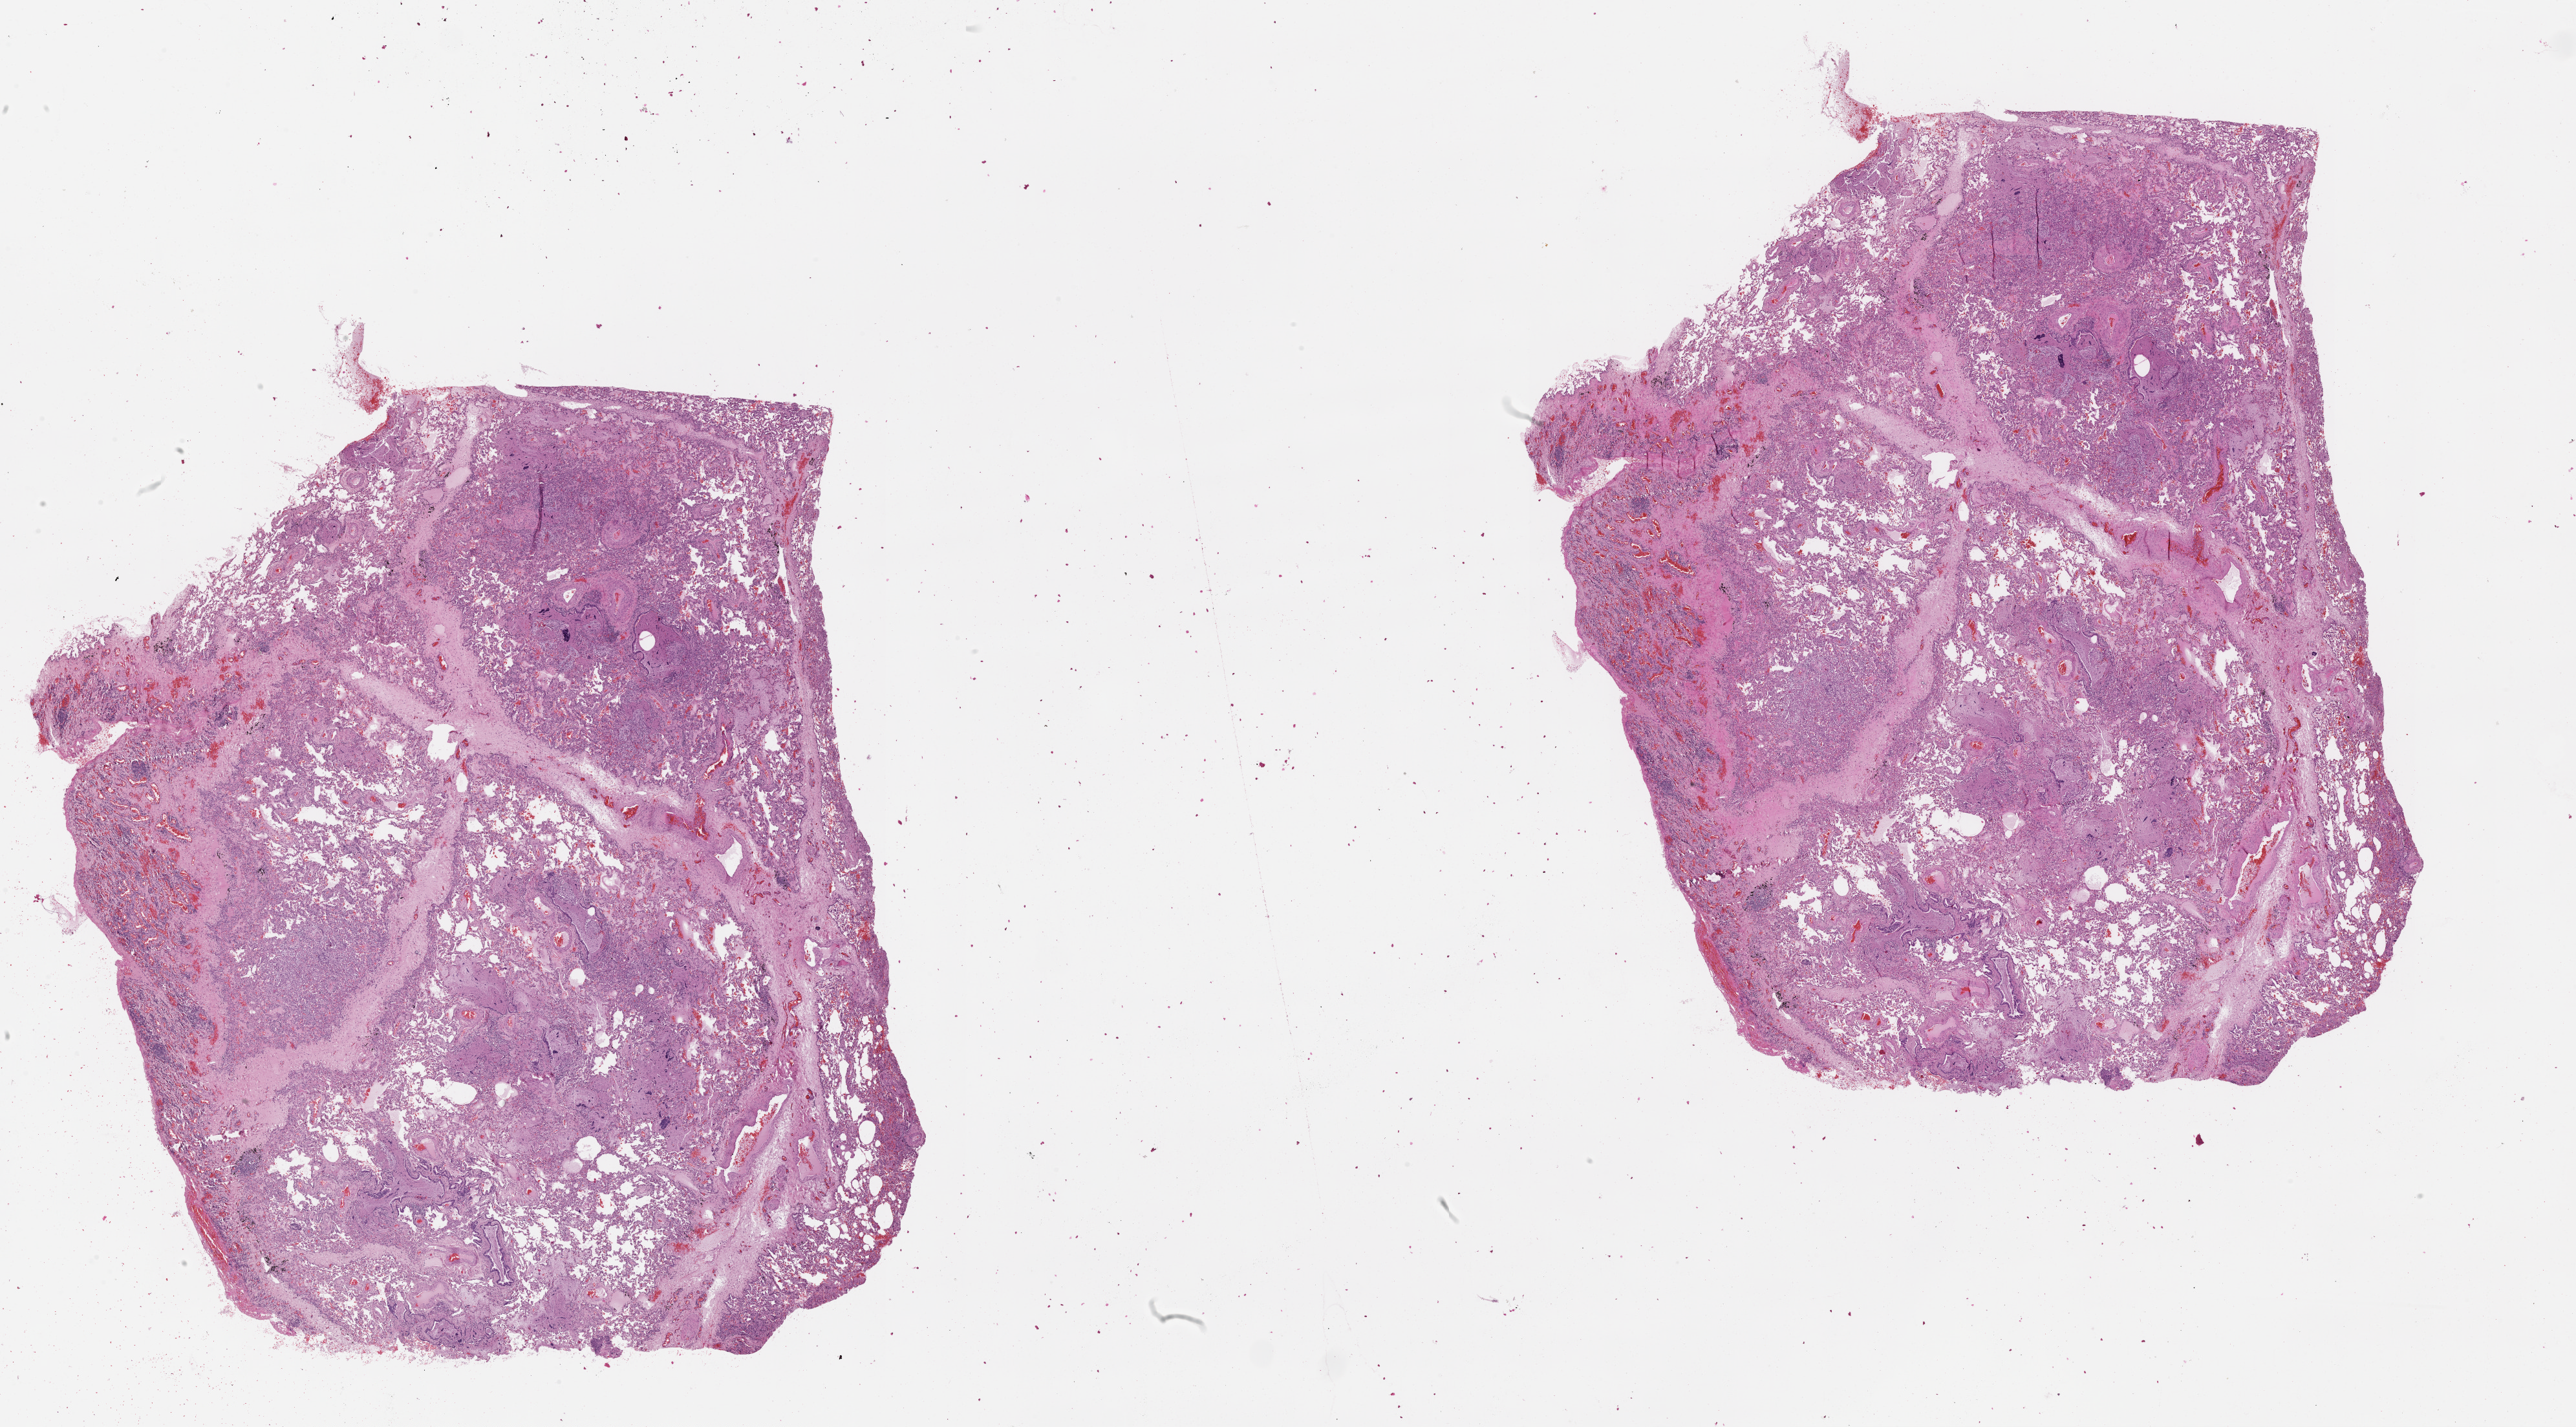
Whole-slide histology image, Hematoxylin and eosin (H&E) stained, shown as a low-resolution overview of the whole scanned area (about 32.1 x 17.8 mm, acquisition: 20x scan). Lung, normal (non-tumour) tissue. Patient: male, age 69 years.
• this section: normal (non-tumour) tissue from the same patient
• patient diagnosis (cohort enrolment): squamous cell carcinoma (lung)